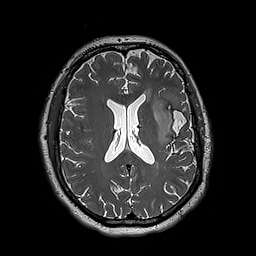
Brain MRI from a brain-tumour surgery series, one axial slice; position 89 of 192 along the scan axis; 1 mm slice thickness; 256 × 256 image matrix, field of view 250 × 250 mm. Case-level facts recorded for this patient, not image findings: histopathology: Astrocytoma; WHO grade: 3; IDH mutation: yes; tumour location: Left Insular.
Outlined on this slice (manually delineated by an expert):
- tumour: bounding box <153,95,179,145> (left, top, right, bottom; pixels)